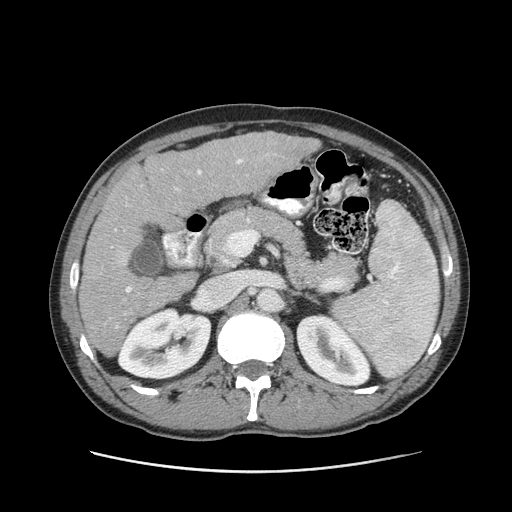
Contrast-enhanced abdominal CT (liver protocol), one axial slice. Slice 46 of 93 in the series (ordered by position). Reconstruction kernel STANDARD. 120 kVp. Soft-tissue window (W 400 / L 40 HU). 512 × 512 image matrix. From the clinical record (not read from this slice): diagnosis: hepatocellular carcinoma (patient treated with transarterial chemoembolisation; whether this scan precedes or follows treatment is not stated here); TNM stage (as recorded): Stage-II; Child-Pugh class: A; tumour differentiation: moderately differentiated; tumour size: 1 cm.
Outlined on this slice (semi-automatic segmentation, software-assisted and operator-edited):
- liver parenchyma outside the tumour (the mass and vessels are separate outlines, so this box may not span the whole liver): bounding box [x1, y1, x2, y2] px = [78, 132, 320, 356]
- liver vessels: [111, 159, 243, 329]